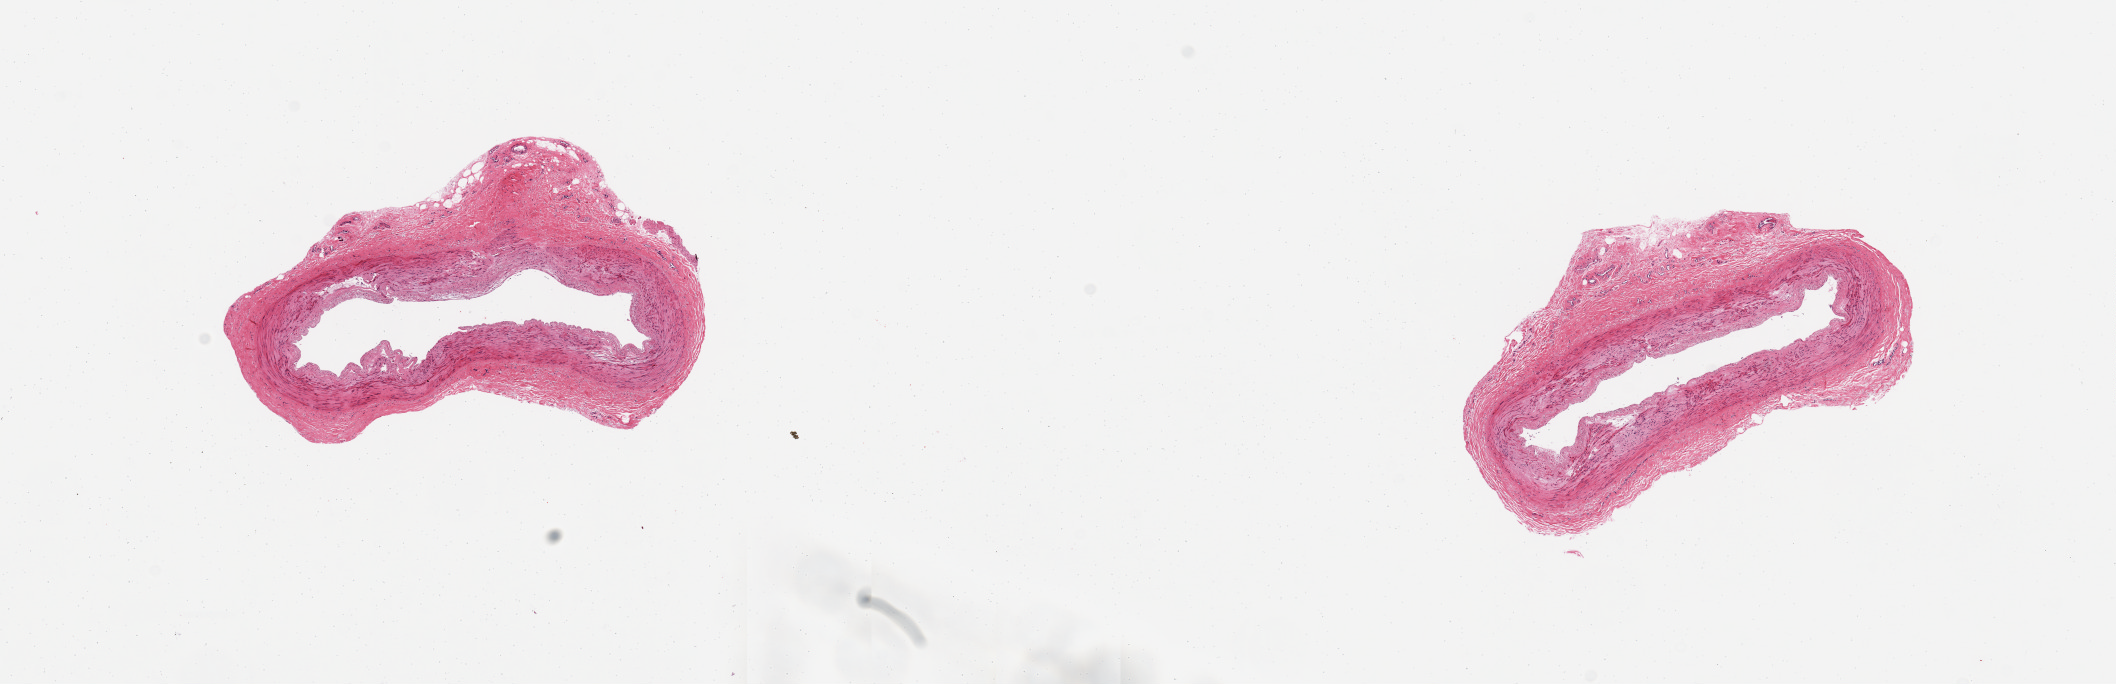
Digitized H&E-stained section, brightfield — a low-resolution overview of the entire scanned area, about 16.7 x 5.4 mm (acquisition: 20x scan), PAXgene-fixed, paraffin-embedded tissue, sampled site (target tissue): tibial artery, donor tissue sample. Donor sex: male.
- reviewer comment on this tissue sample: 2 pieces; well trimmed